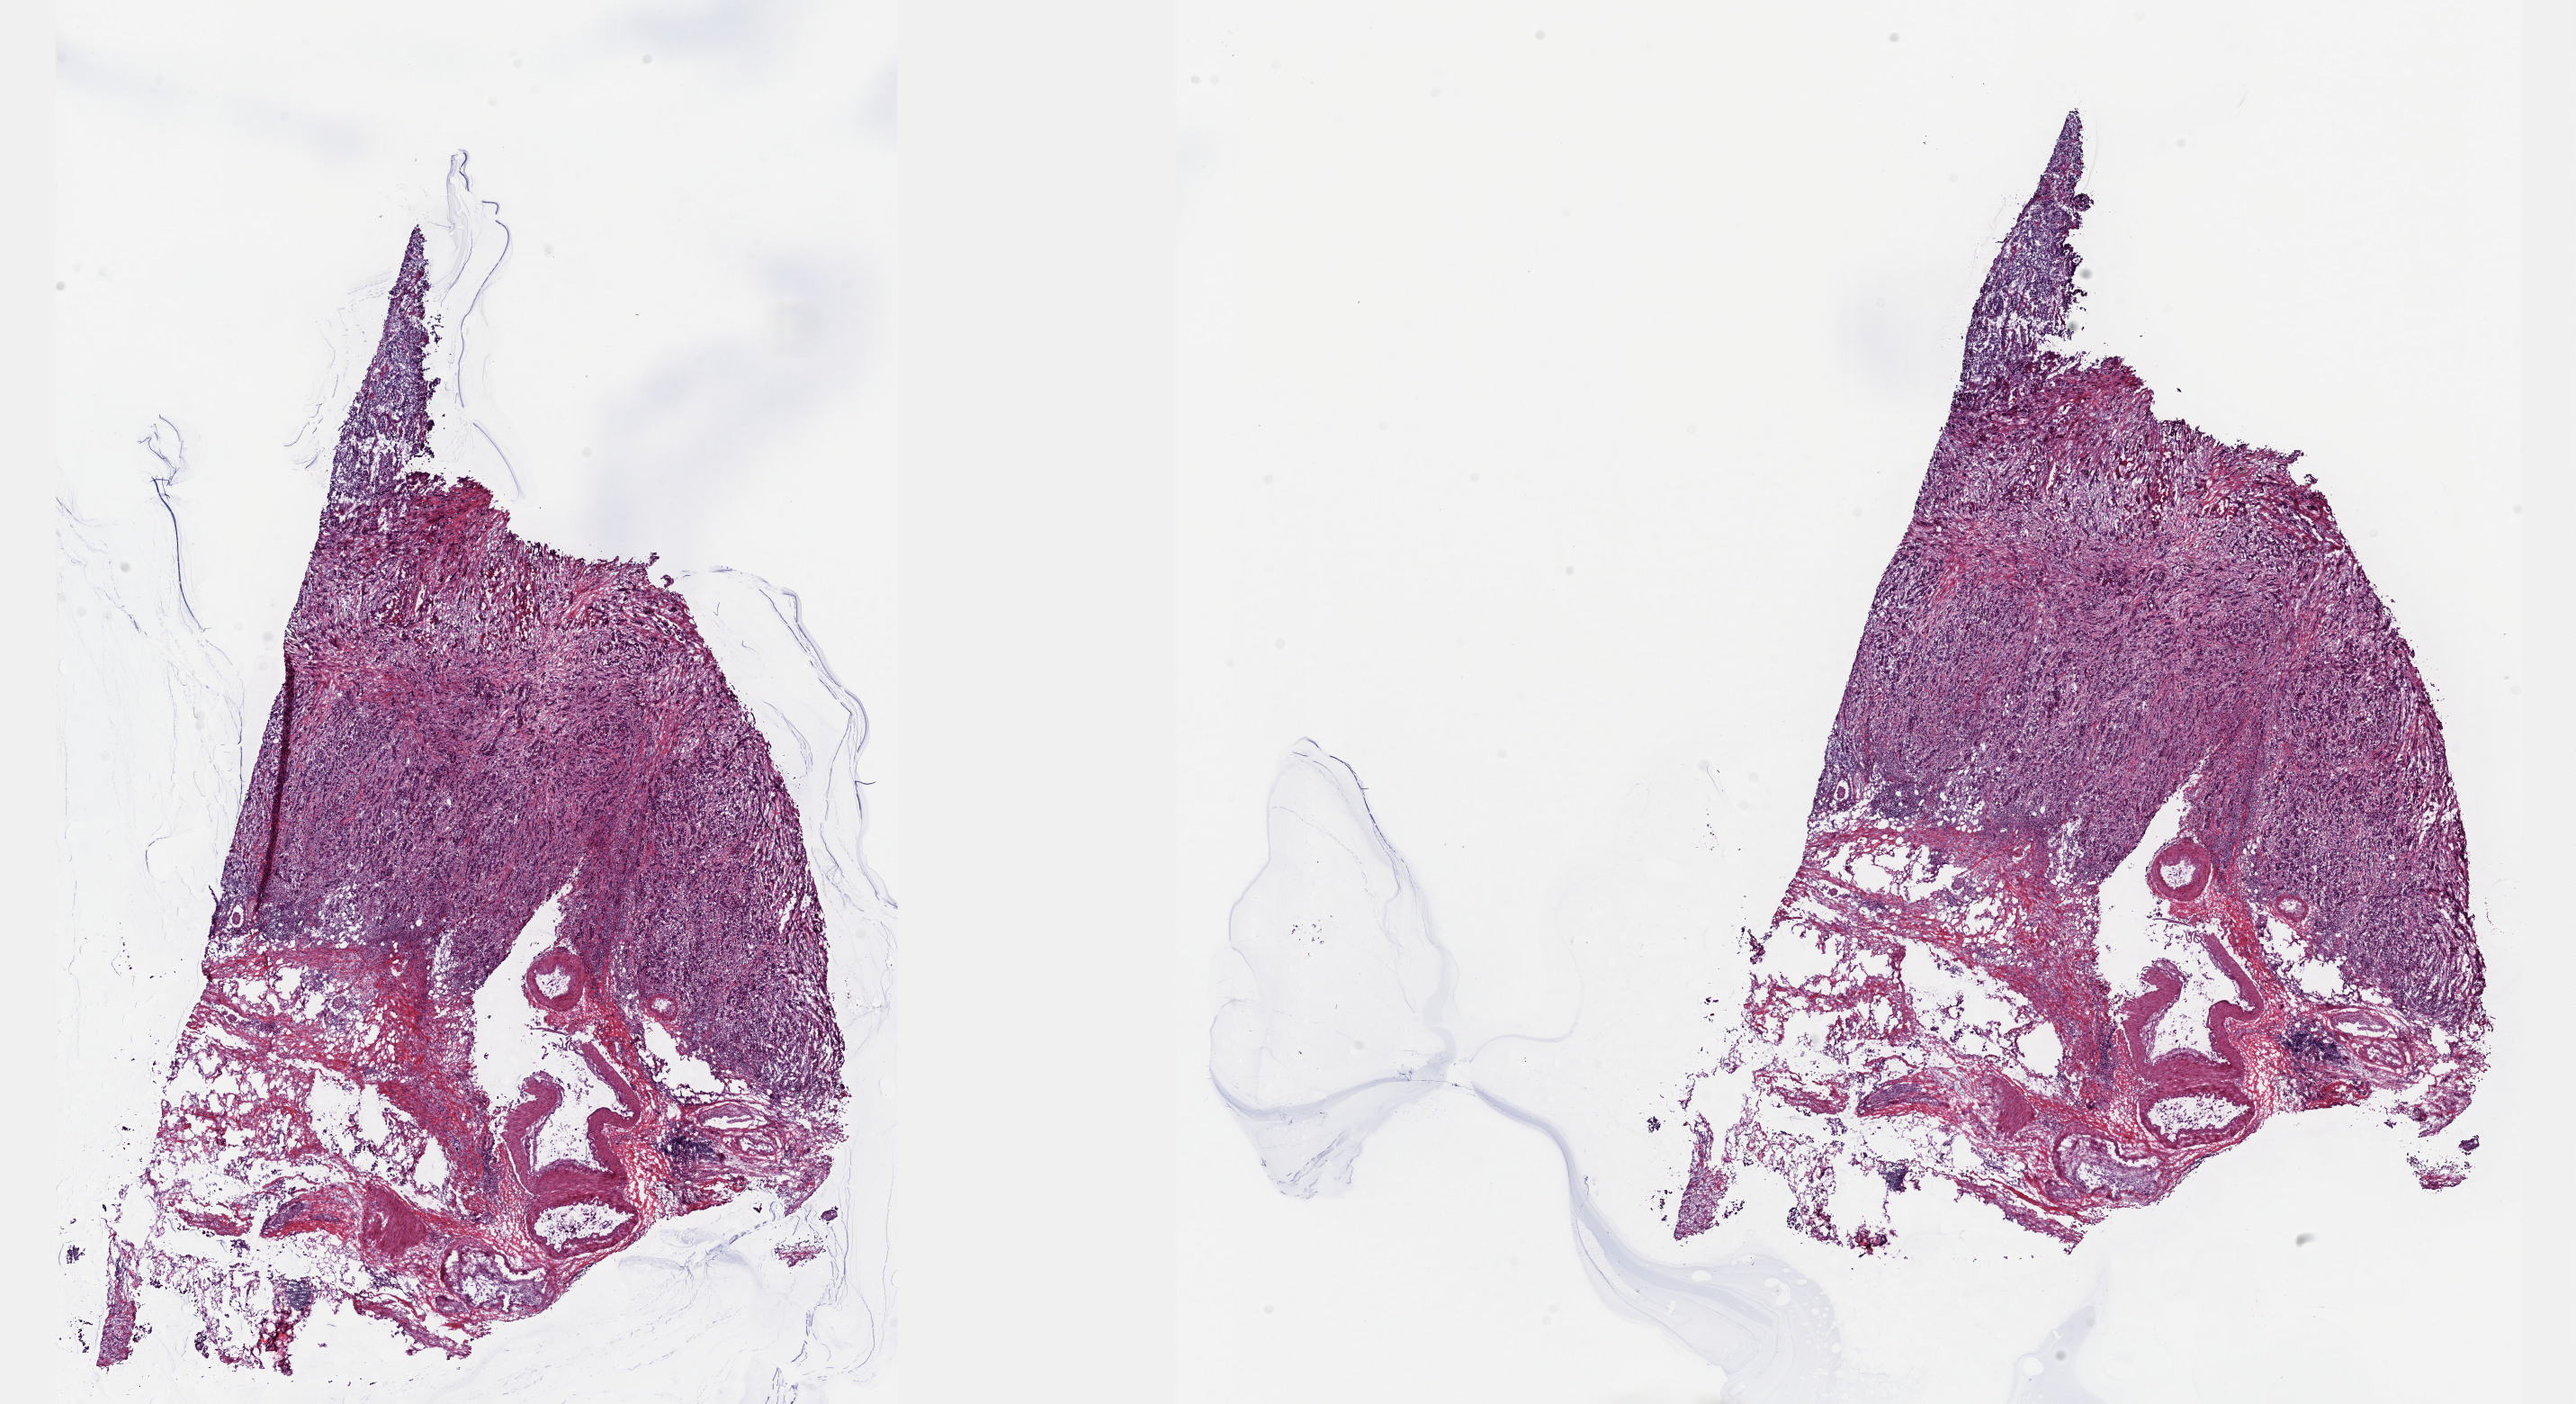
Whole-slide histology image, H&E, low-resolution overview of the scanned area, about 23.1 x 12.6 mm. Frozen section. Sample: primary tumour, bladder. Male patient; age at initial diagnosis 83 years. Slide review estimates, as recorded: tumour cells 75%, tumour nuclei 75%.
Diagnosis: Transitional cell carcinoma.